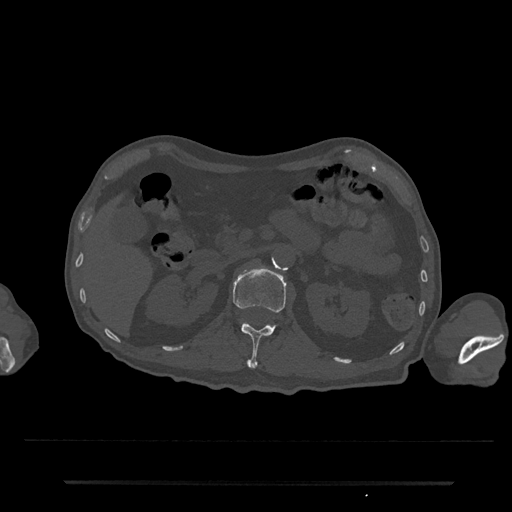
CT including the spine, one axial slice; slice 119 of 797 in the series (ordered by position); bone window (W 1800 / L 400 HU); 0.5 mm slice thickness; 512 × 512 image matrix, field of view 427 × 427 mm. Male patient, age 74 years. Case-level facts recorded for this patient, not image findings: primary cancer: prostate.
Annotated regions visible in this slice (semi-automatic segmentation, software-assisted and operator-edited):
- L1 vertebra: bounding box [x1, y1, x2, y2] px = [233, 267, 286, 369]